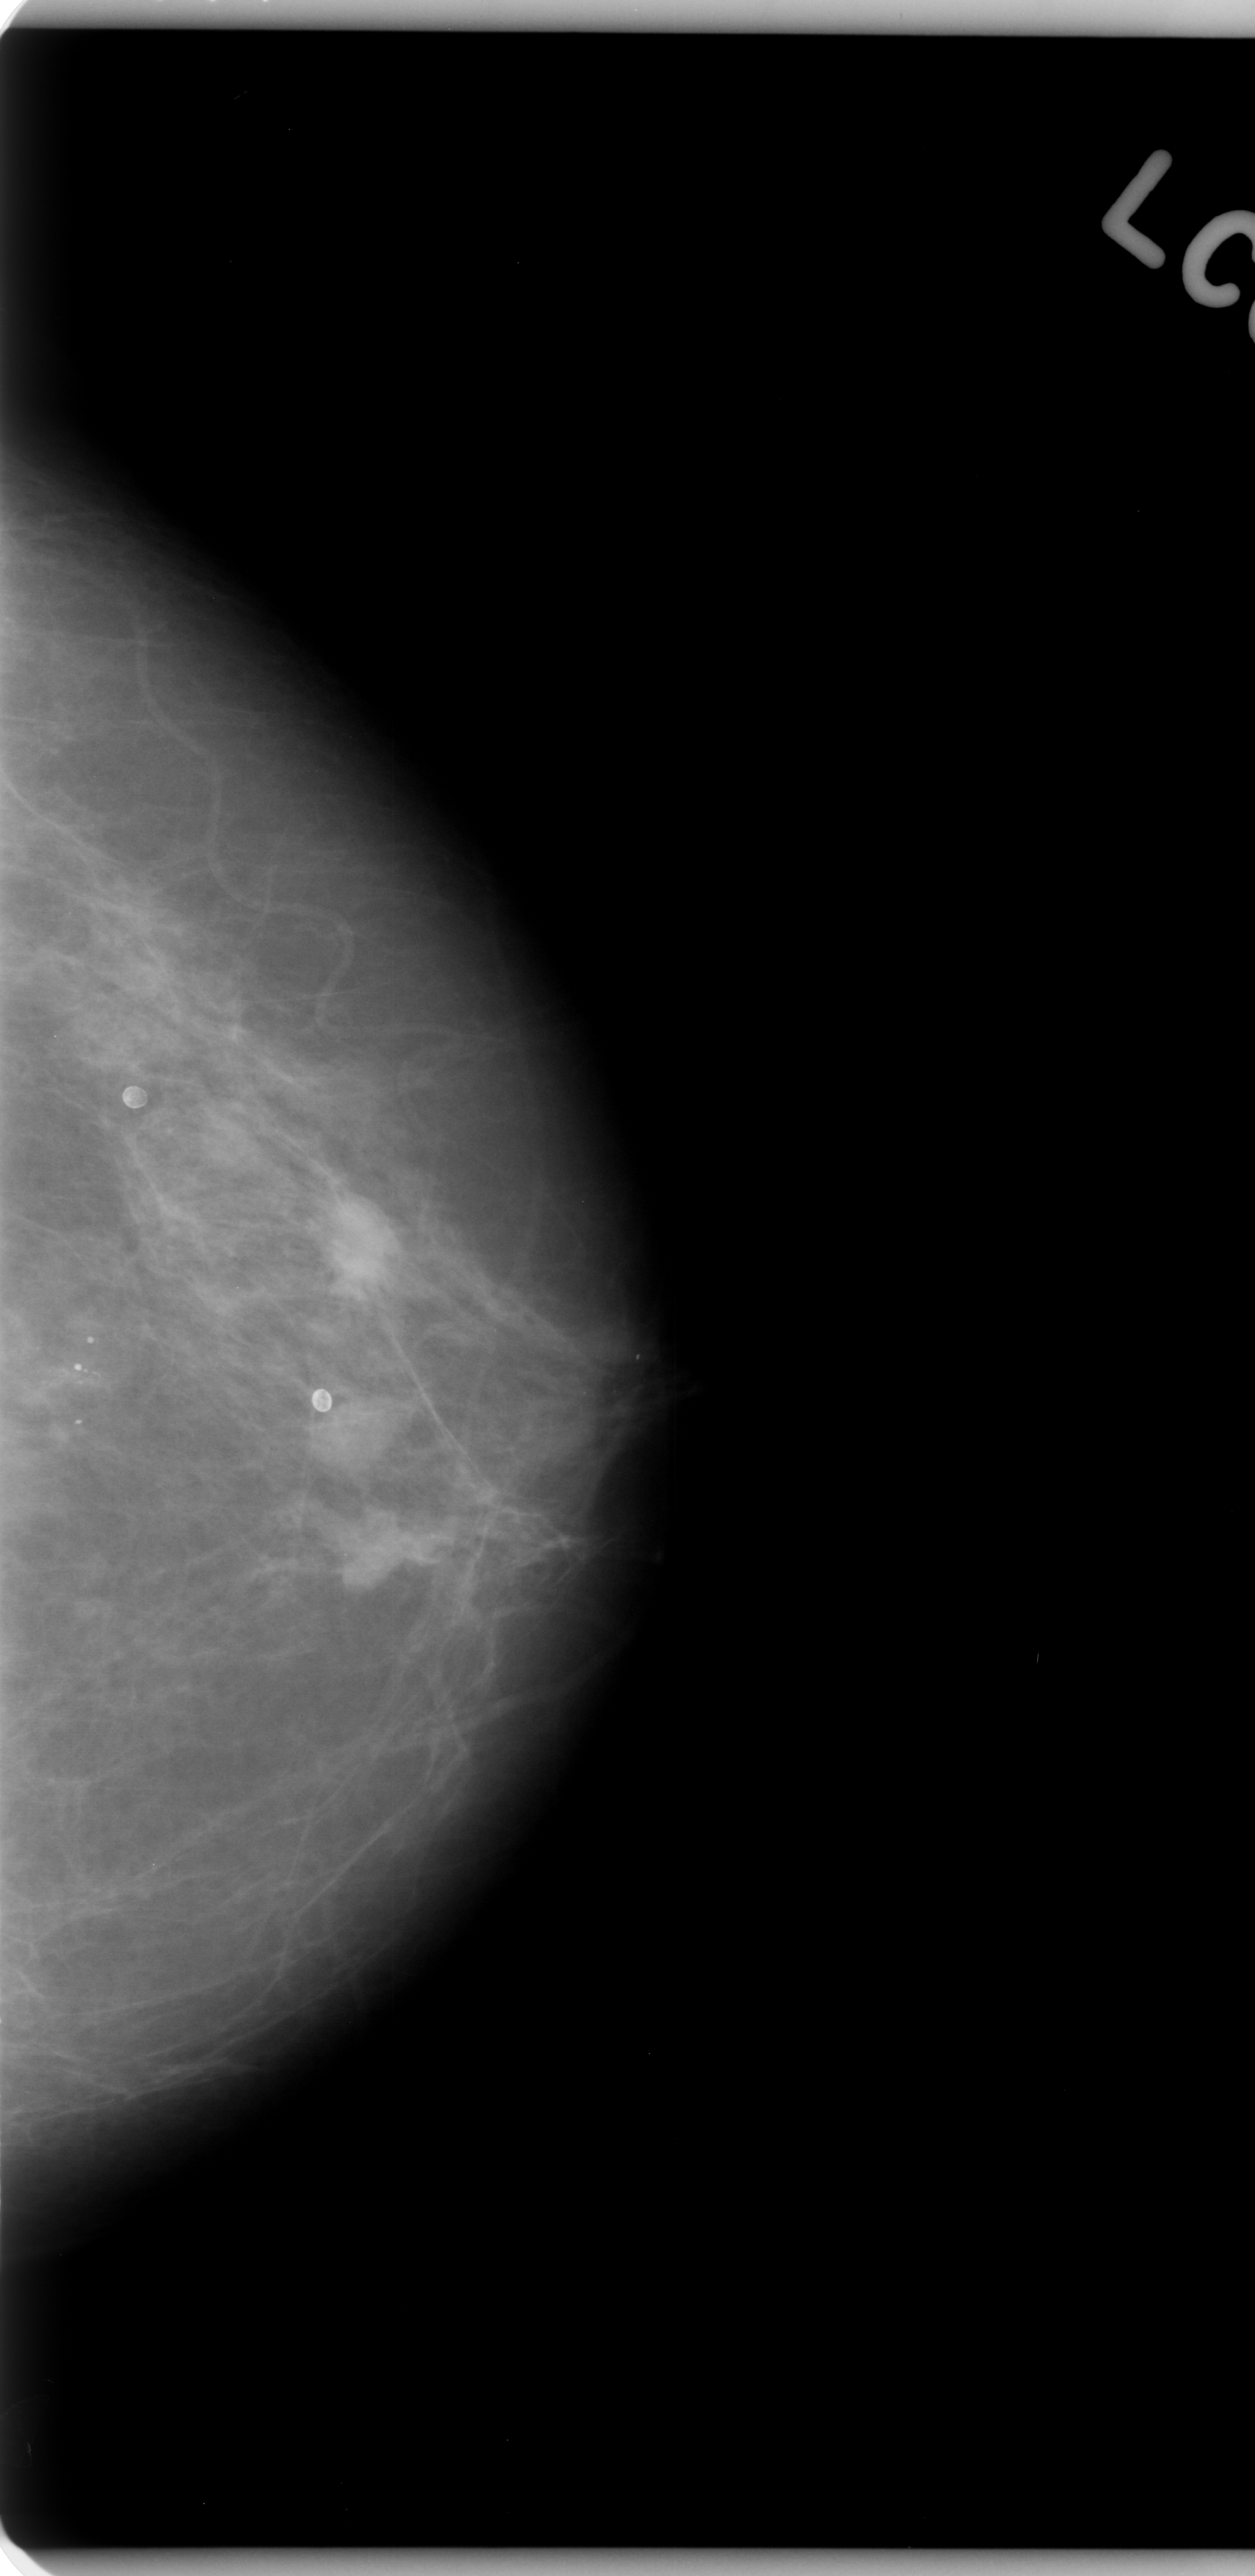
Mammogram (digitized film), left breast, CC view, breast composition: almost entirely fatty (BI-RADS density category 1 of 4).
- Abnormality record for this image: Finding 1 of 3: mass, shape oval, margins microlobulated; BI-RADS assessment category 4; subtlety rating 5 on a 1 (subtle) to 5 (obvious) scale; pathology result (as recorded, not read from the image): malignant.
- Finding 2 of 3: mass, shape oval, margins microlobulated; BI-RADS assessment category 4; pathology (as recorded): malignant.
- Finding 3 of 3: mass, shape oval, margins microlobulated; BI-RADS assessment category 4; subtlety rating 5 on a 1 (subtle) to 5 (obvious) scale; pathology (as recorded): malignant.